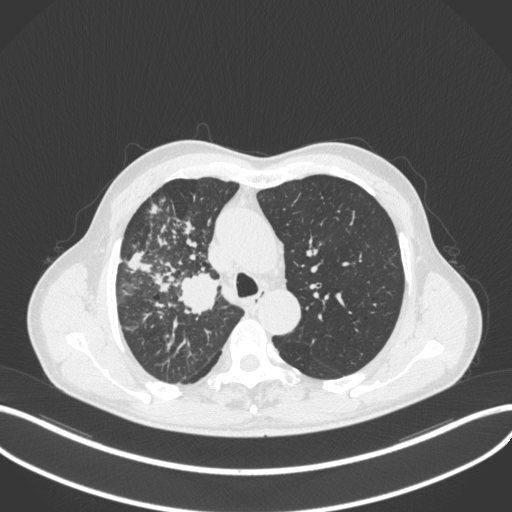
Chest CT, one axial slice. Slice 342 of 490 in the series (ordered by position). 120 kVp. Lung window (W 1500 / L -600 HU). 1 mm slice thickness. 512 × 512 image matrix. Male patient, age 69 years. Case-level facts recorded for this patient, not image findings: clinical TNM (as recorded): T2a N0 M0.
Outlined on this slice (rectangle marked by the reading radiologist):
- lung tumour (recorded histology: adenocarcinoma): bounding box <178,271,223,314> (left, top, right, bottom; pixels)